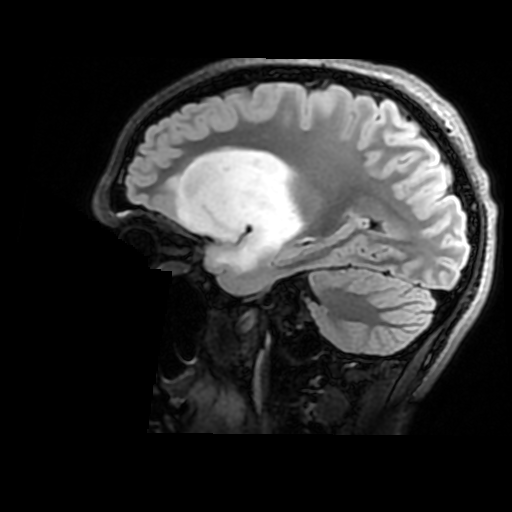
Brain MRI from a brain-tumour surgery series, one sagittal slice. Slice 114 of 176 in the series (ordered by position). T2 FLAIR. 1 mm slice thickness. 512 × 512 image matrix, field of view 240 × 240 mm. Case-level facts recorded for this patient, not image findings: histopathology: Astrocytoma; WHO grade: 2; IDH mutation: yes.
Annotated regions visible in this slice (manually delineated by an expert):
- tumour: box from (x=179, y=147) to (x=302, y=276) px